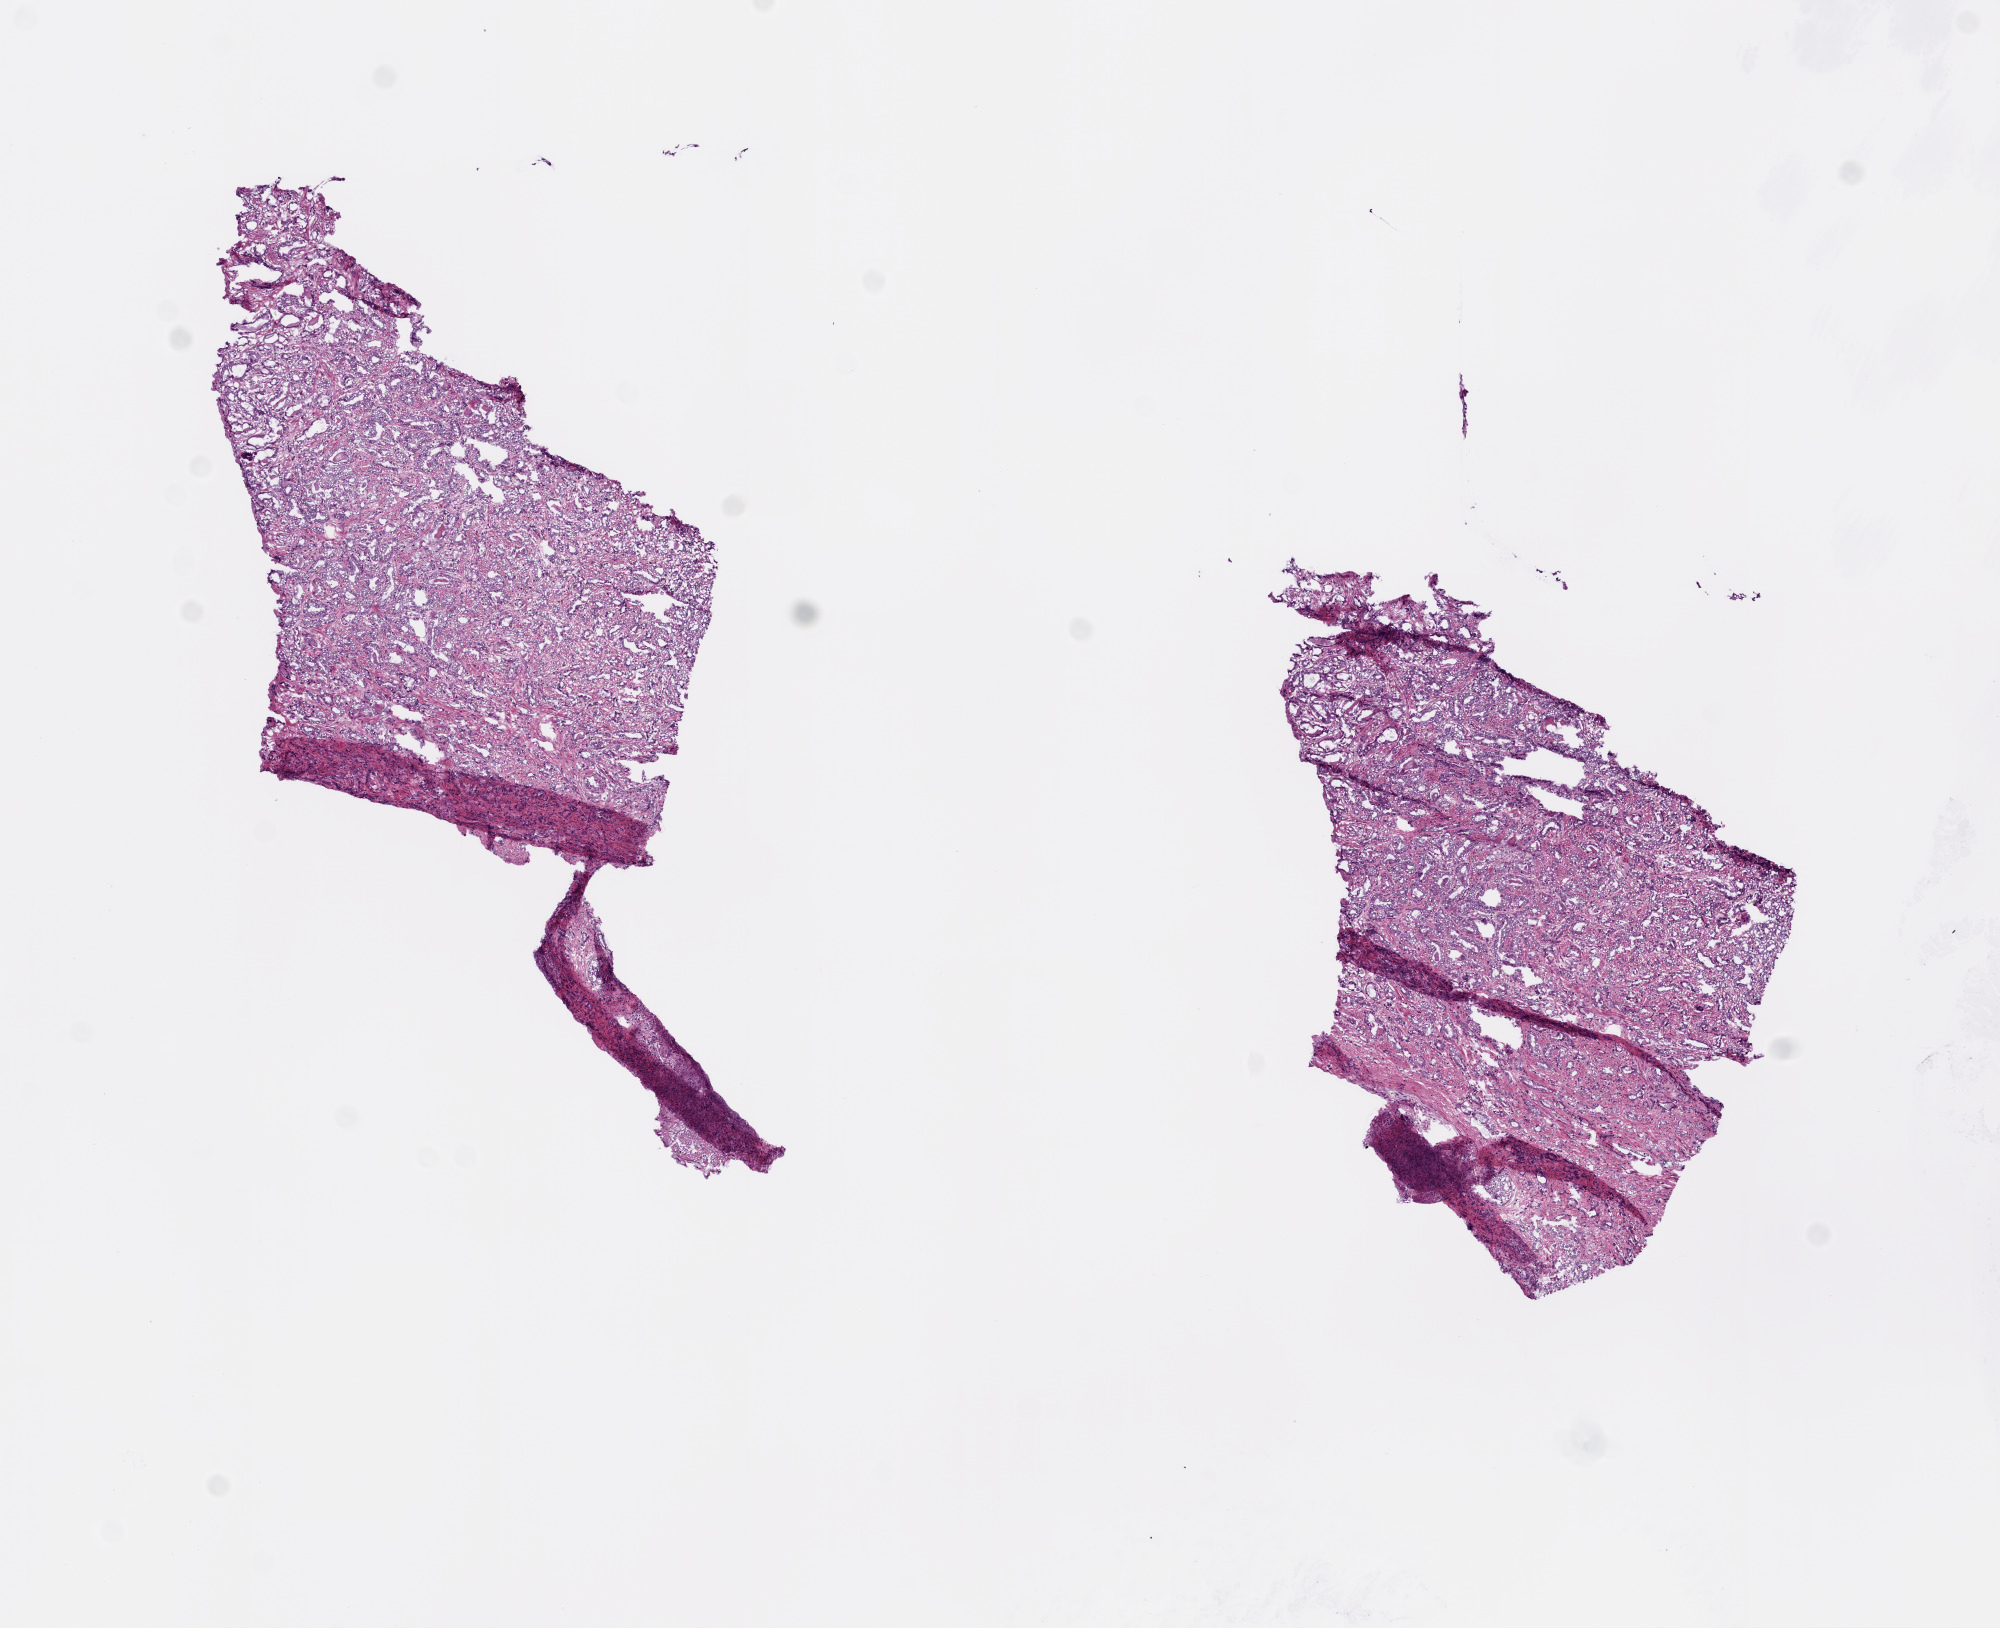
Digitized Hematoxylin and eosin (H&E) stained tissue section (whole slide) — low-resolution overview of the scanned area, about 8.0 x 6.5 mm. Frozen section from the bottom of the tissue portion. Primary tumour sample from the prostate. Male patient; age at initial diagnosis 68 years. Gleason score: 7 (3+4). Slide review estimates, as recorded: tumour cells 65%, tumour nuclei 75%, normal cells 2%, stromal cells 33%, necrosis 0%. Inflammatory infiltration, as recorded: lymphocyte infiltration 0%, monocyte infiltration 0%, neutrophil infiltration 0%.
- histologic diagnosis: Acinar cell carcinoma (prostate gland)
- lymph nodes positive (case pathology): 0 of 5 examined